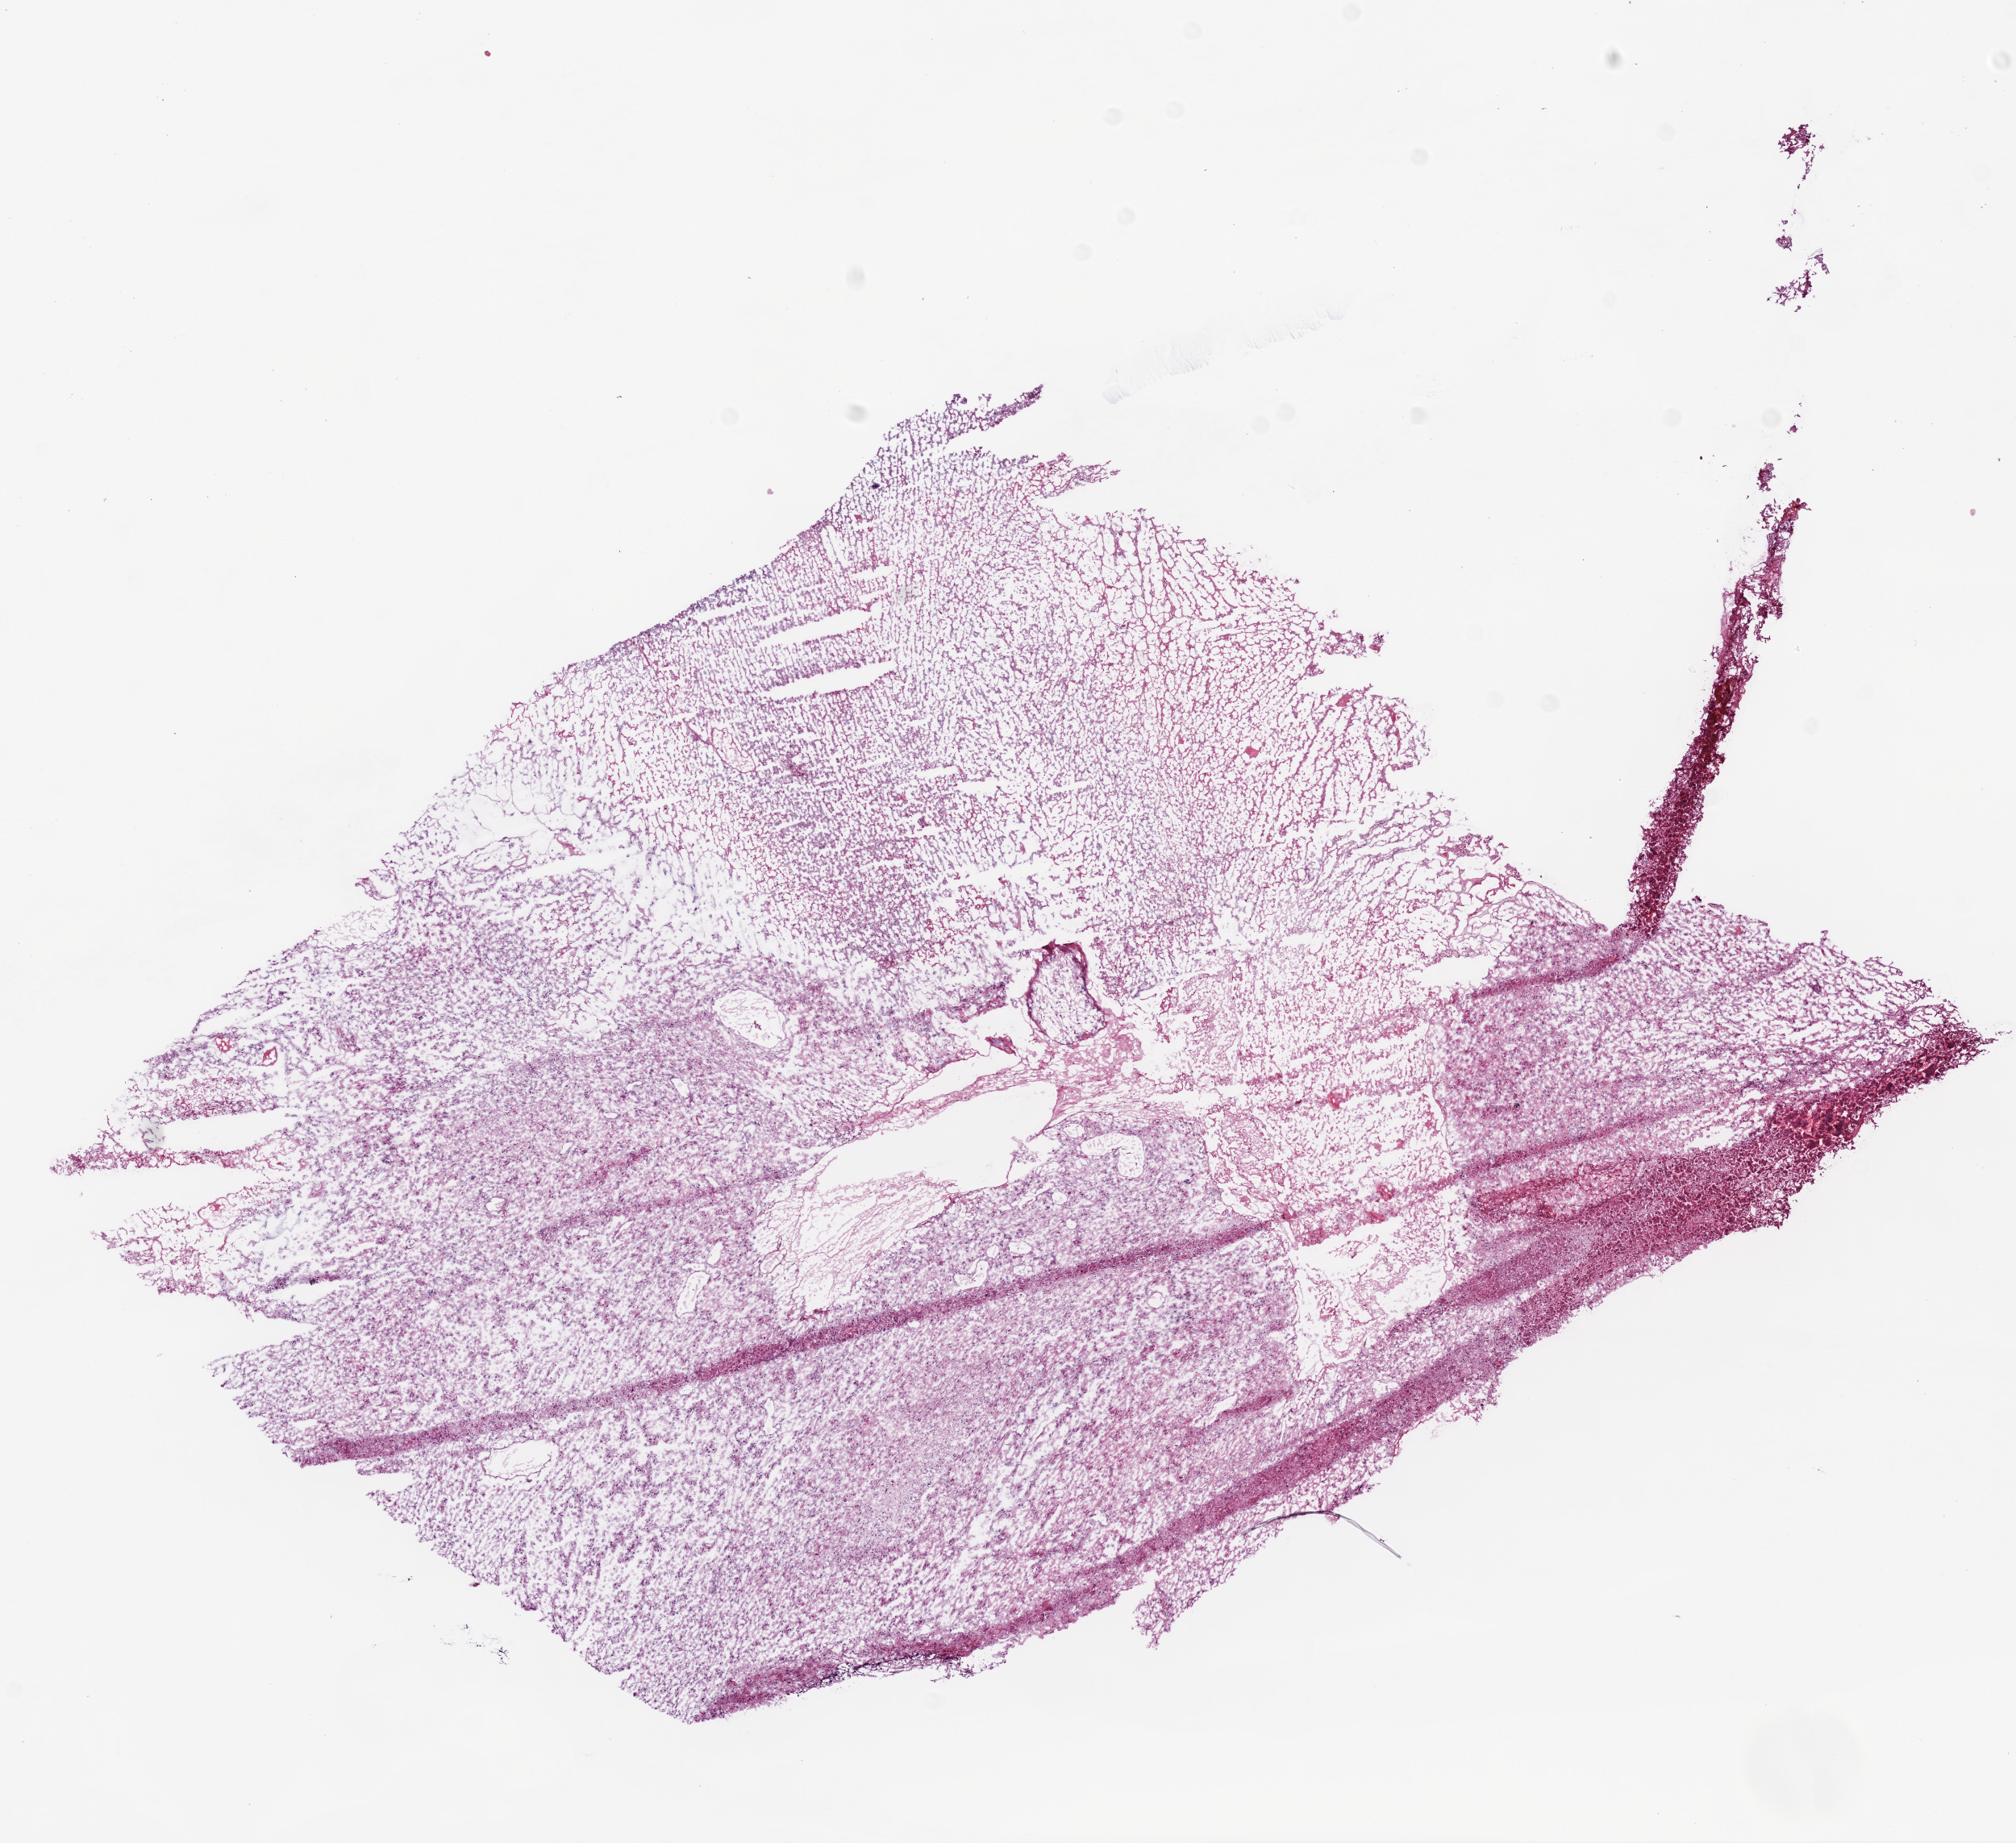
Digitized Hematoxylin and eosin (H&E) stained tissue section (whole slide), whole scanned area (about 10.0 x 9.2 mm, from a 20x scan) shown as a low-resolution overview. Frozen section from the bottom of the tissue portion. Sample: primary tumour, brain. Male patient; age at initial diagnosis 57 years. Slide review estimates, as recorded: tumour cells 60%, tumour nuclei 90%, normal cells 0%, stromal cells 10%, necrosis 30%.
- diagnosis: Glioblastoma